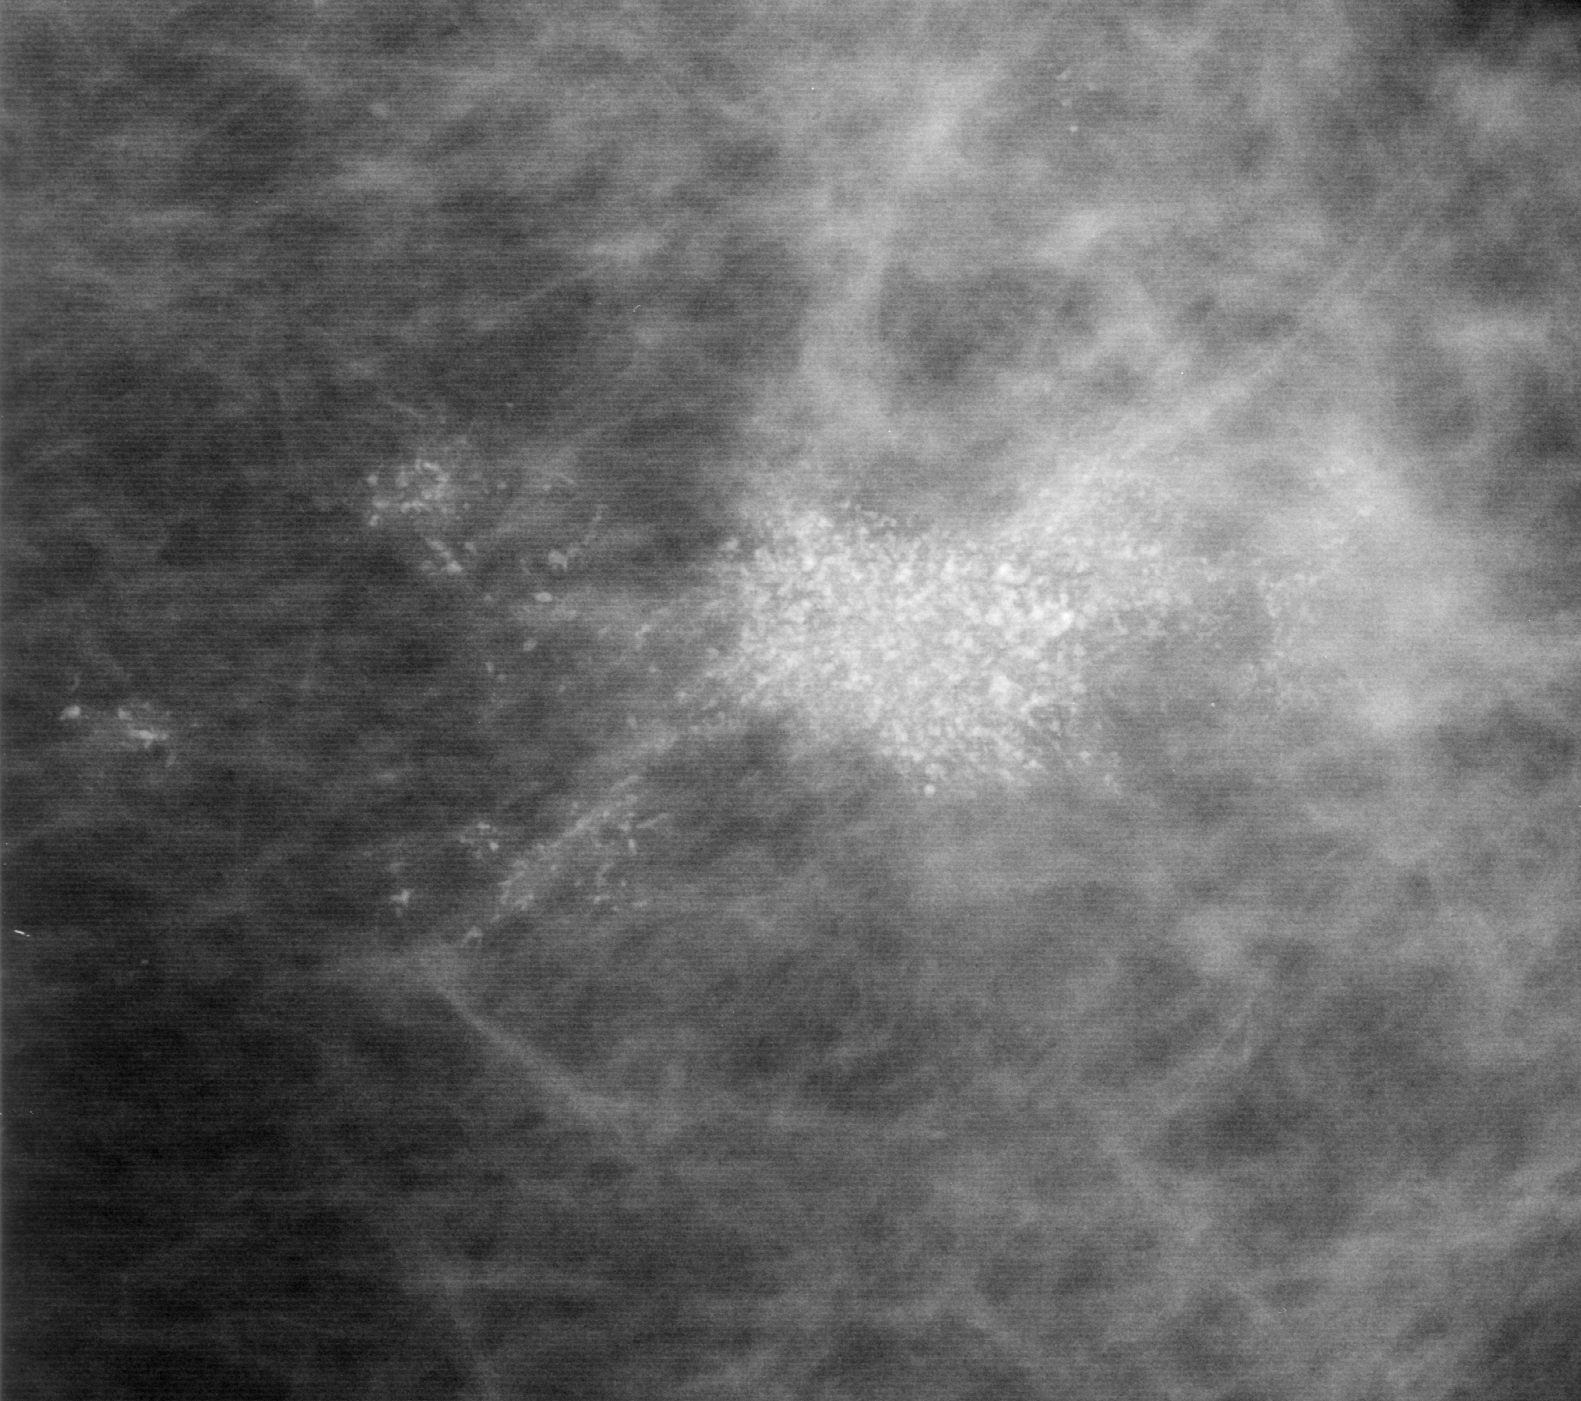
Cropped region of a digitized screen-film mammogram centred on a radiologist-marked abnormality; left breast; CC view.
Finding: calcifications, morphology pleomorphic, distribution segmental; BI-RADS assessment category 5; subtlety rating 5 on a 1 (subtle) to 5 (obvious) scale; pathology result (as recorded, not read from the image): malignant.